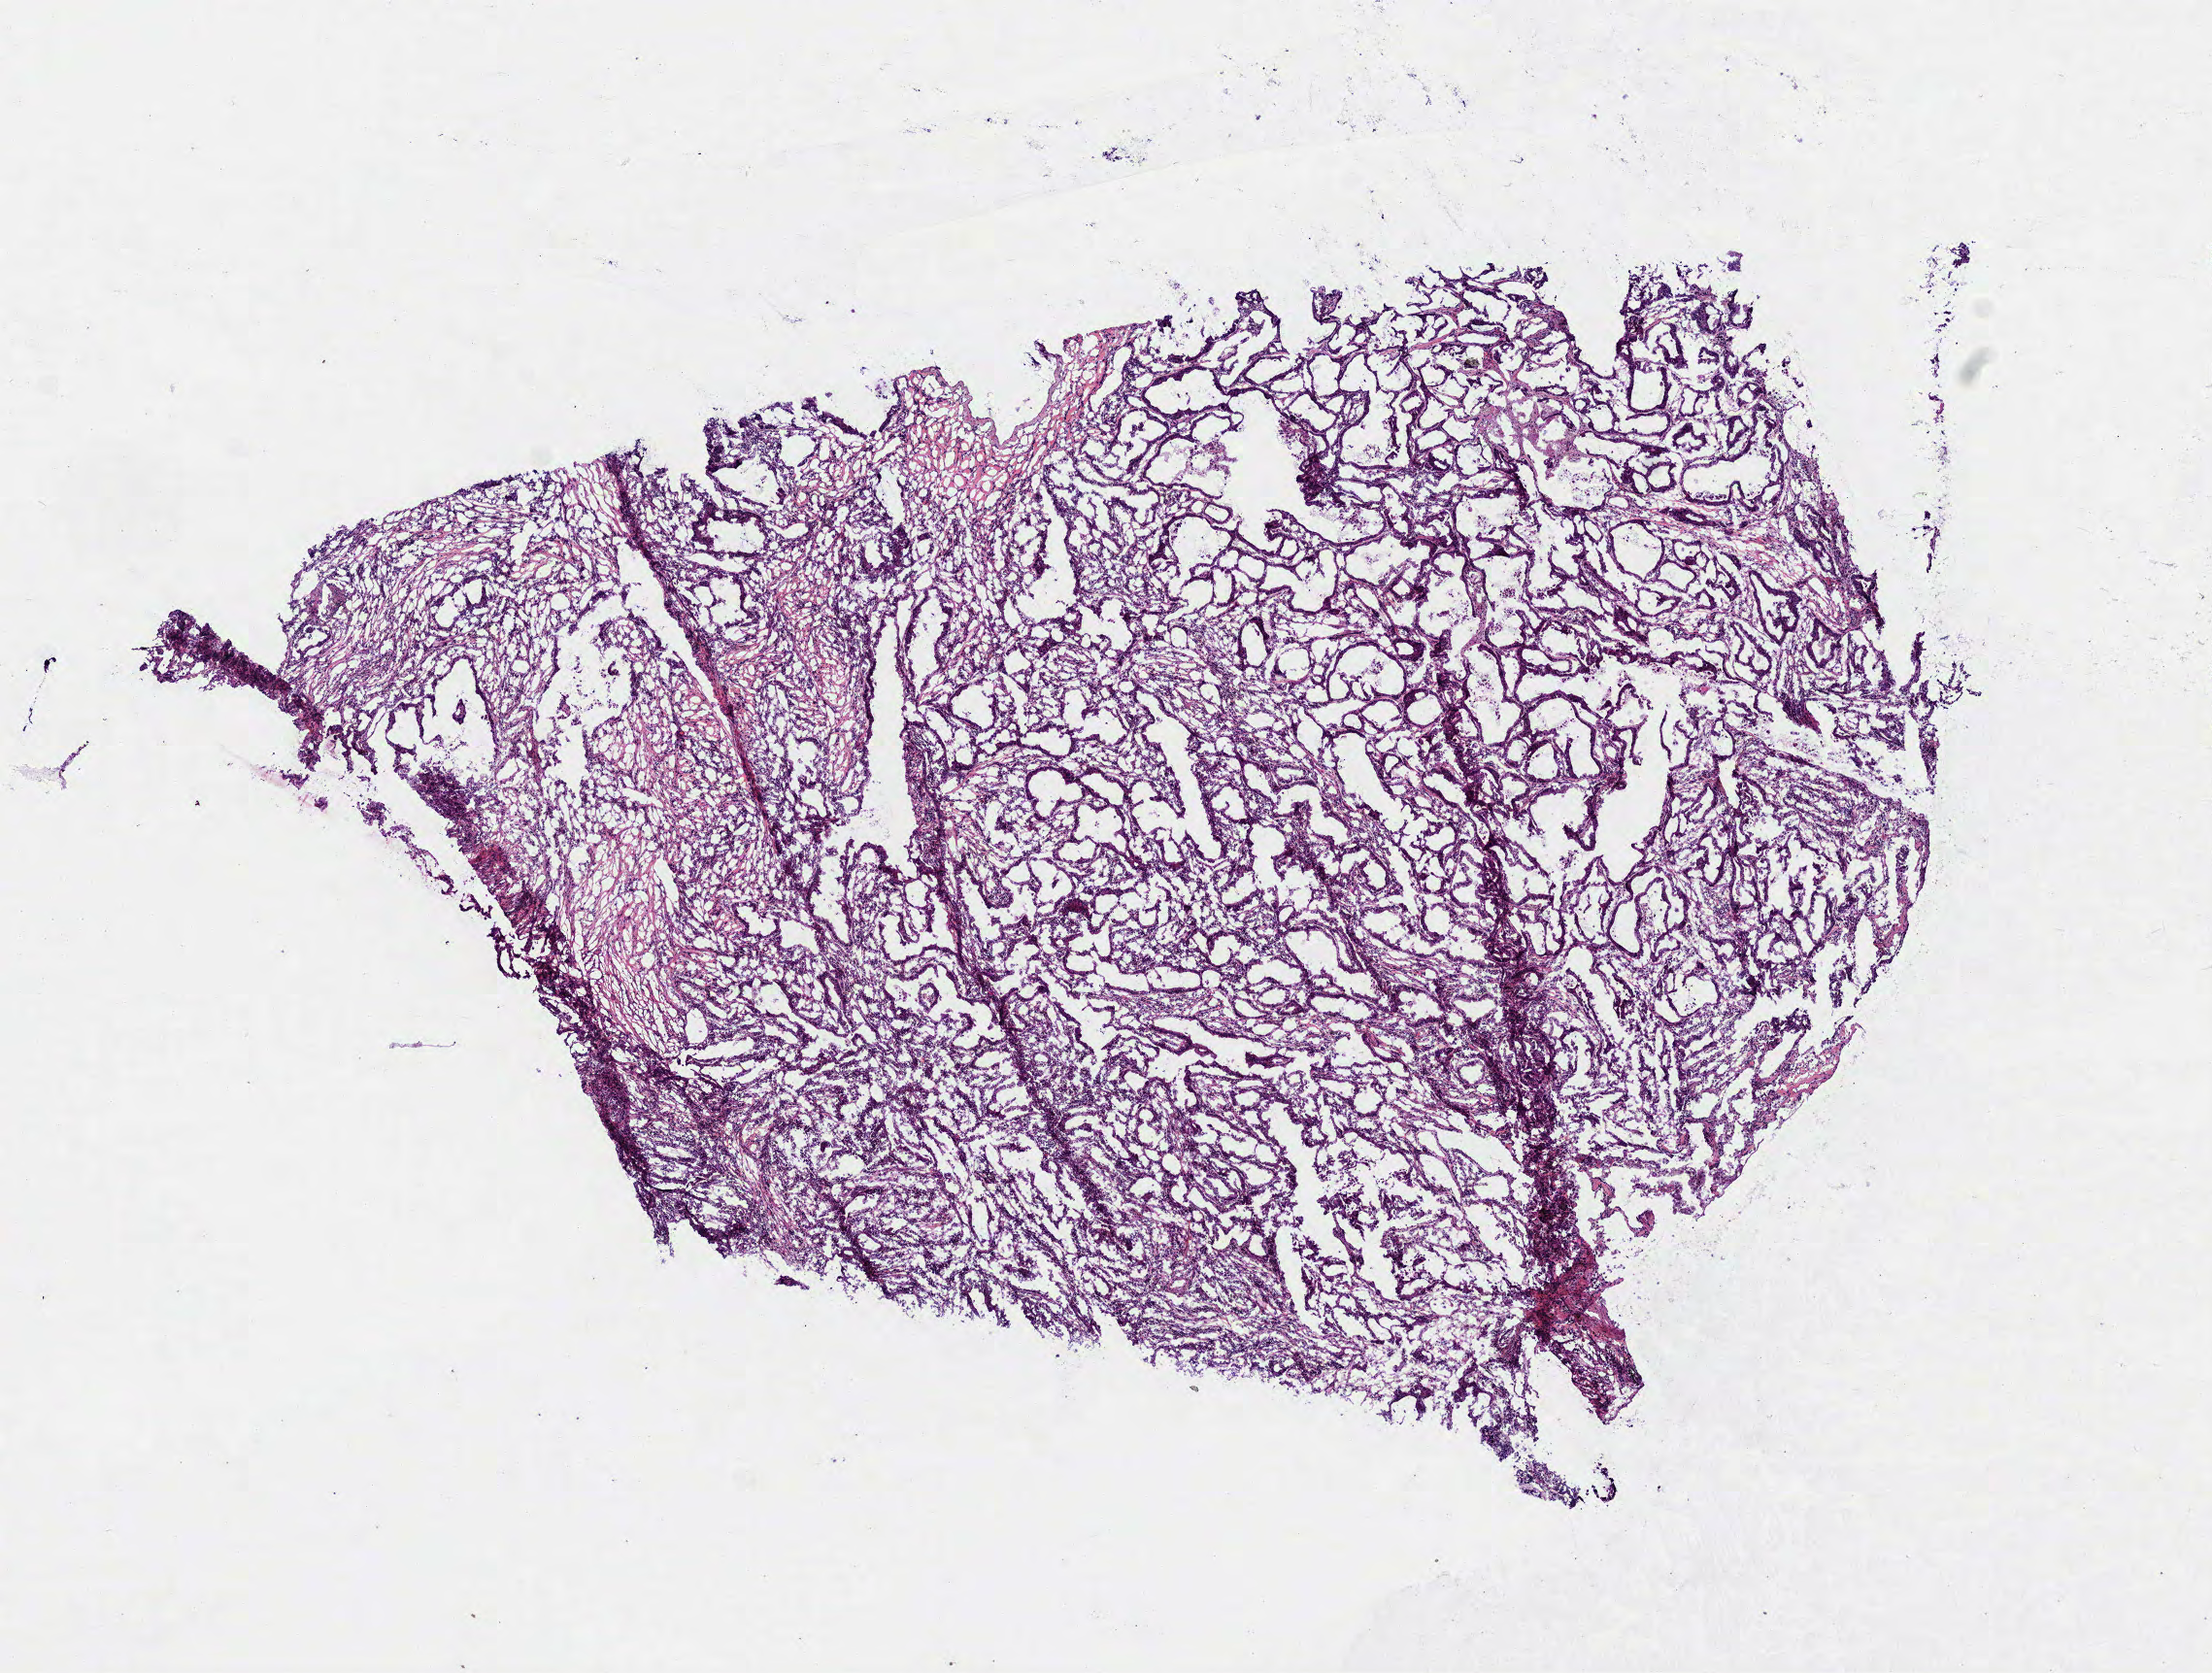
Digitized Hematoxylin and eosin (H&E) stained tissue section (whole slide) — shown as a low-resolution overview of the whole scanned area (about 9.2 x 6.9 mm, from a 40x scan); frozen section from the top of the tissue portion; primary tumour sample from the lung. Female, age 51 years at initial diagnosis. Pathologist review of this section (percent, as recorded): tumour cells 95%, tumour nuclei 62%, normal cells 5%, stromal cells 0%, necrosis 0%. Infiltration values recorded for this section: lymphocyte infiltration 20%, monocyte infiltration 0%, neutrophil infiltration 0%.
- pathologic diagnosis: Bronchiolo-alveolar carcinoma, non-mucinous
- laterality: right
- AJCC pathologic stage: IIIB (6th edition)